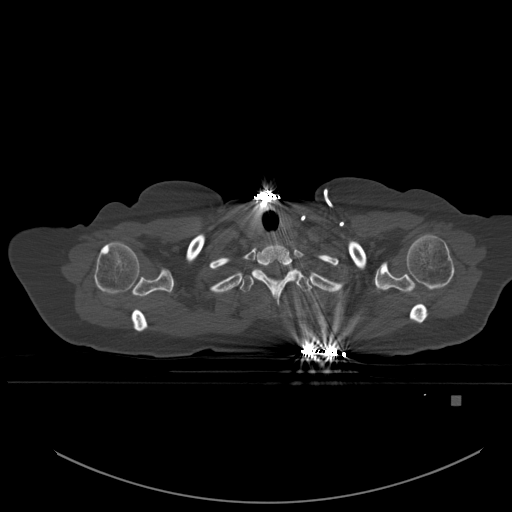
CT including the spine, one axial slice. Bone window (W 1800 / L 400 HU). 512 × 512 image matrix, field of view 443 × 443 mm. Female patient, age 49 years. From the clinical record (not read from this slice): primary cancer: breast; vertebrae with lytic lesions (as recorded): L3, T12, L4.
Structures marked on this image (semi-automatic segmentation, software-assisted and operator-edited):
- T1 vertebra: box from (x=240, y=270) to (x=312, y=295) px